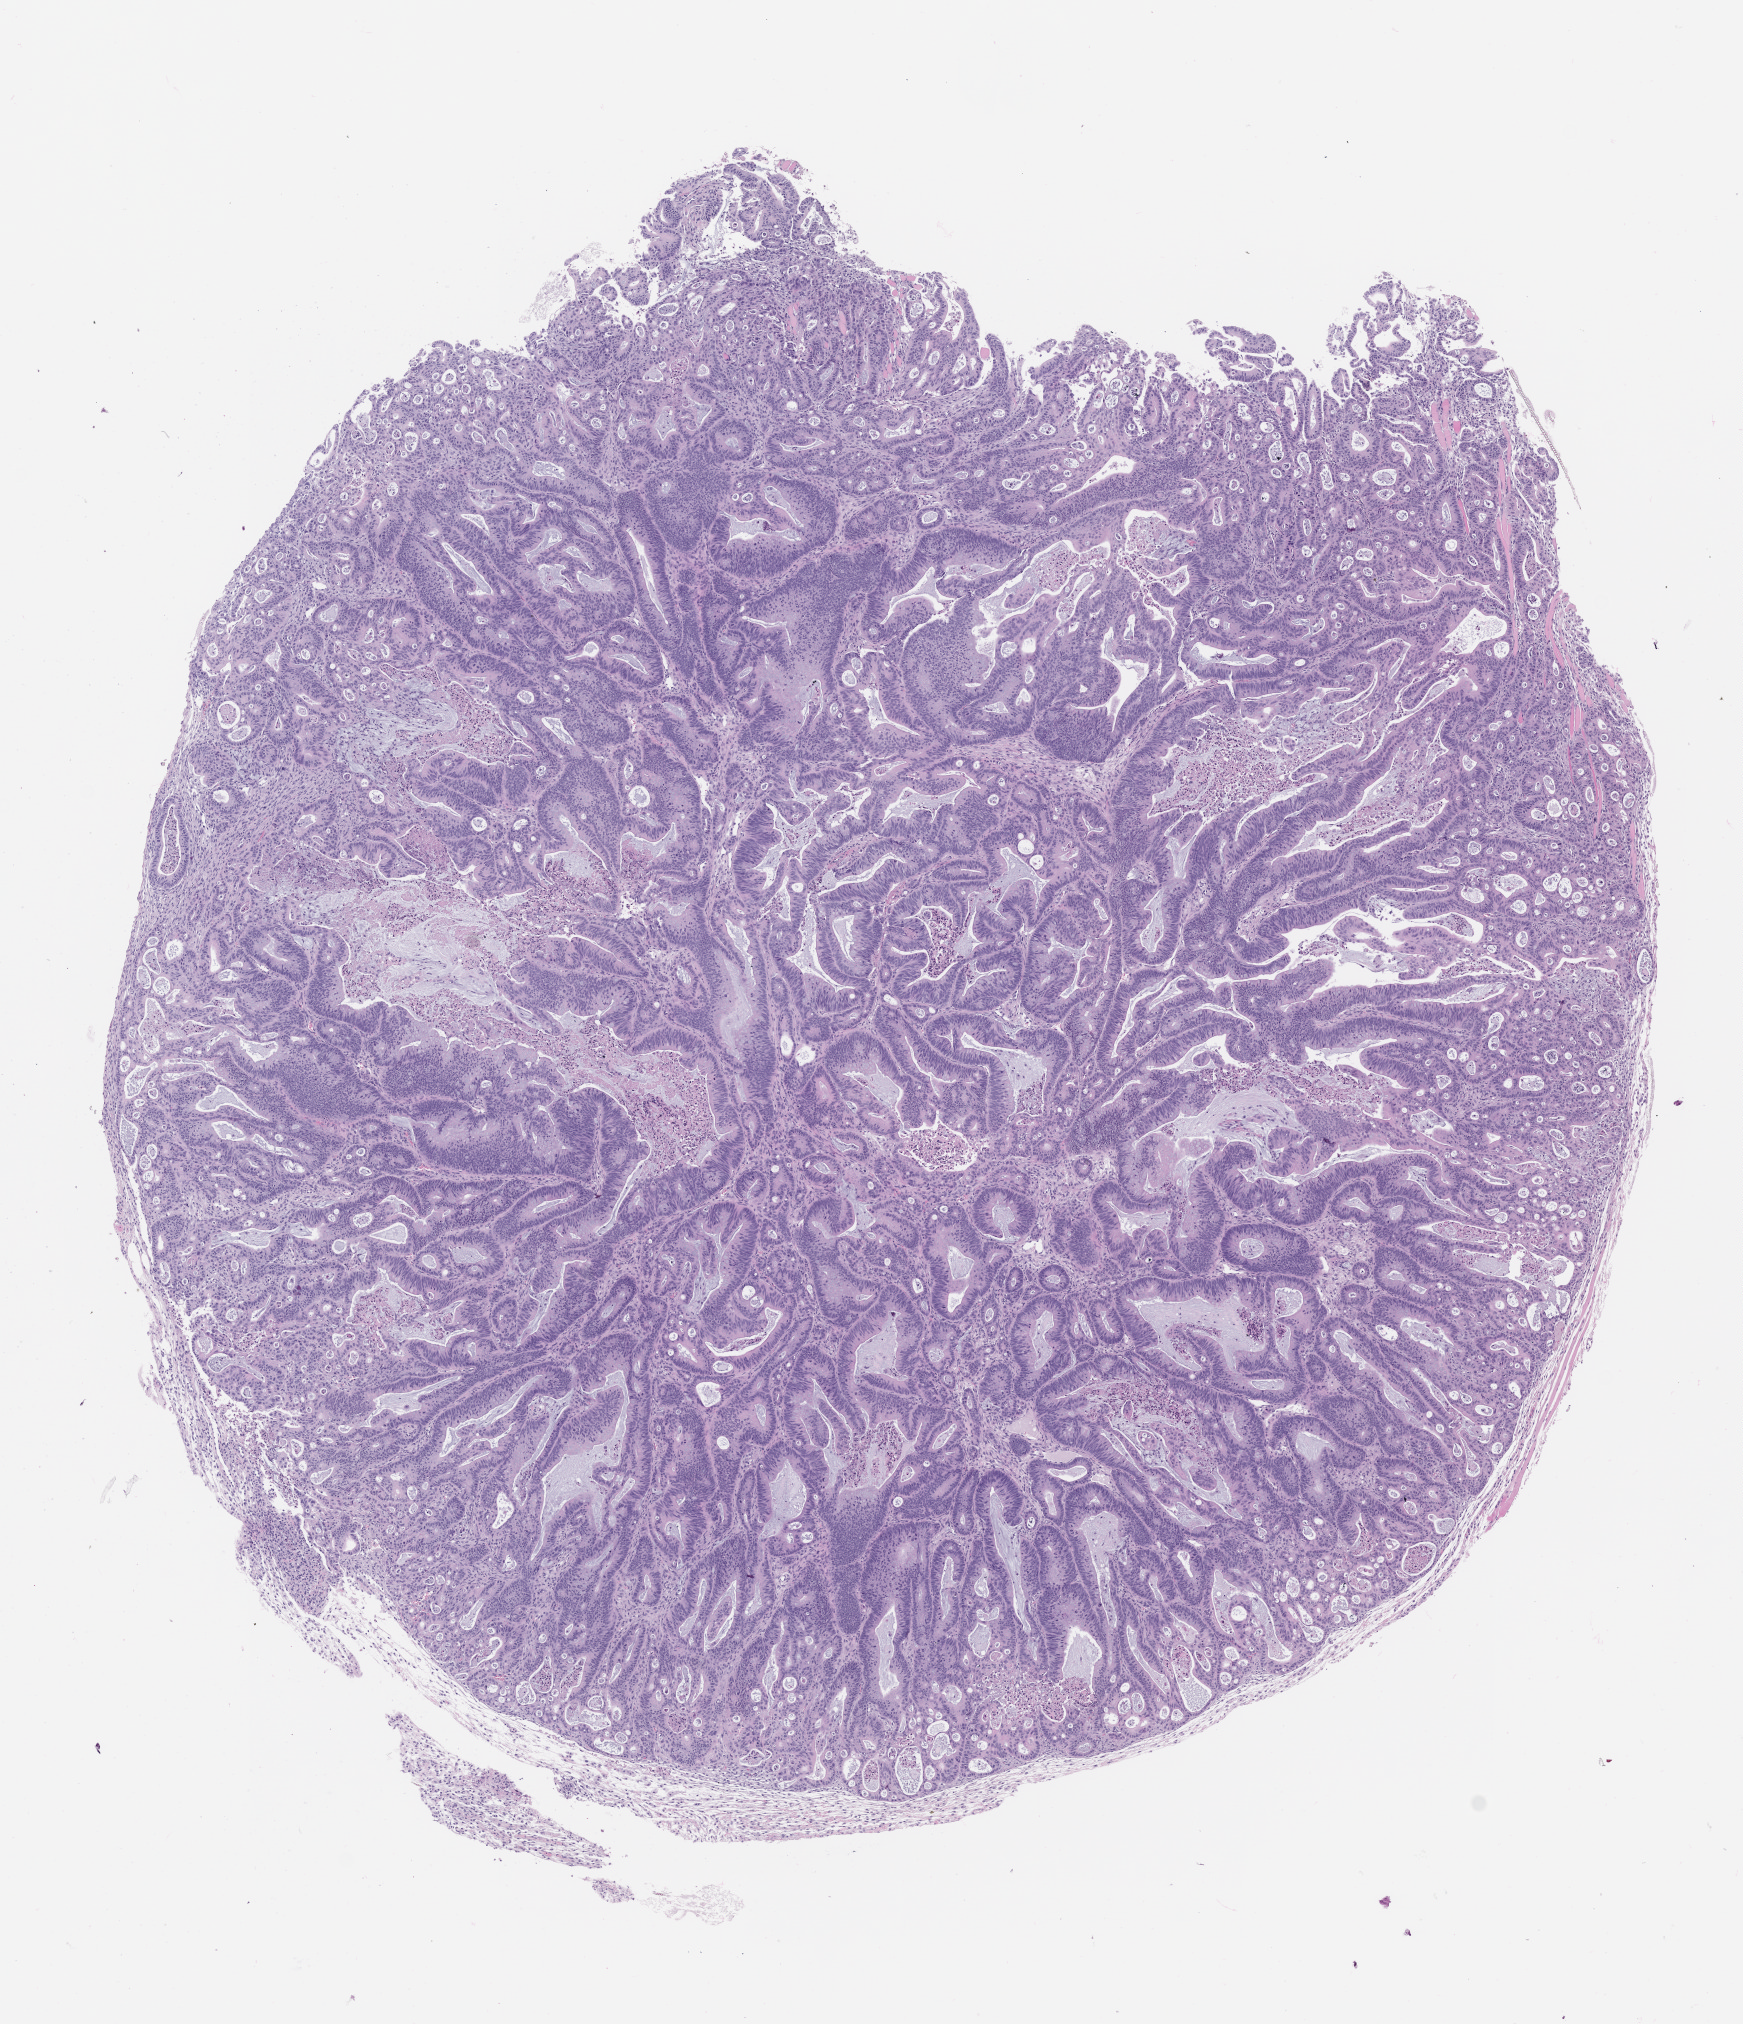
Whole-slide image, H&E: patient-derived xenograft (human tumor grown in a mouse), passage 1 — shown as a low-resolution overview of the whole scanned area (about 7.0 x 8.1 mm). Formalin-fixed paraffin-embedded section. Tumor site category: colon.
Originating patient diagnosis: Colon Adenocarcinoma.